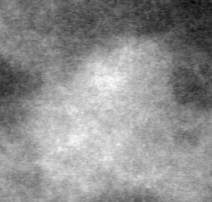
Cropped region of a digitized screen-film mammogram centred on a radiologist-marked abnormality; right breast; CC view.
- Marked abnormality: mass, shape lobulated, margins obscured; BI-RADS assessment category 4; subtlety rating 2 on a 1 (subtle) to 5 (obvious) scale; pathology result (as recorded, not read from the image): malignant.